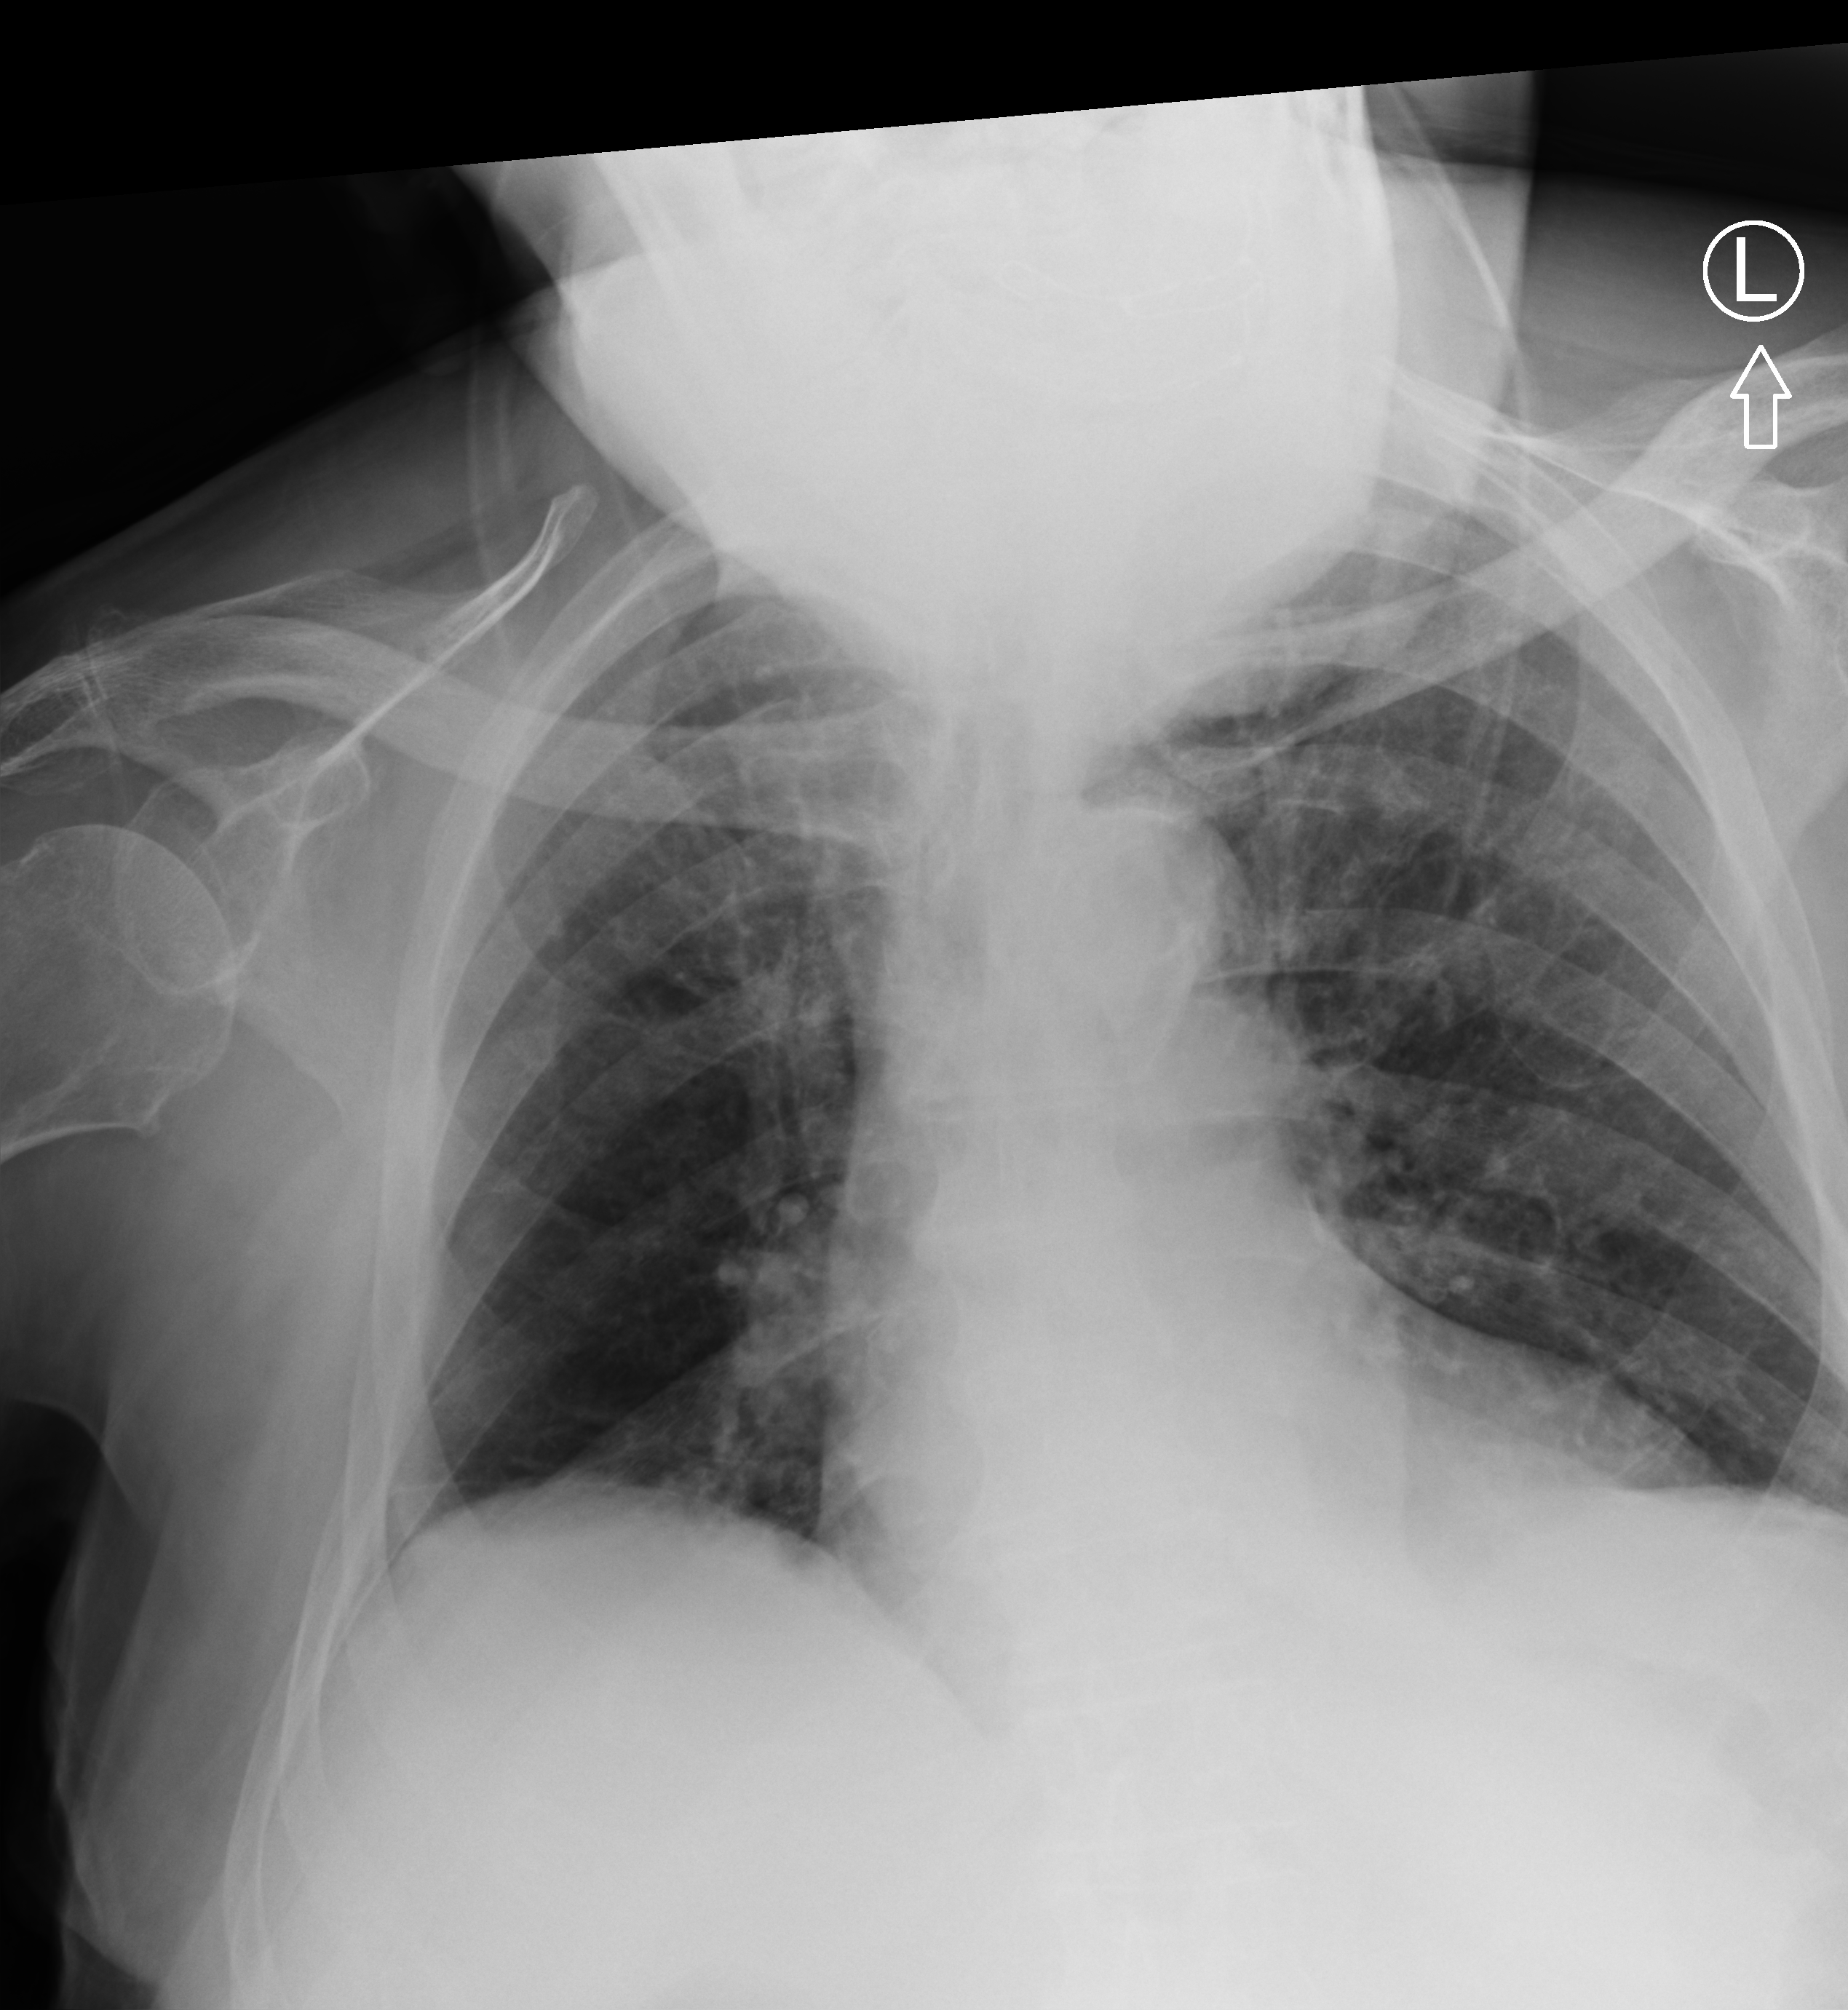
Portable chest radiograph; anteroposterior (AP) projection. Patient hospitalised with COVID-19; male, aged 75–90 years.
Hospital-stay facts (about this admission, not read from this image; timing relative to this image not recorded): COPD (admission record): no; mechanically ventilated during this hospital stay: yes.